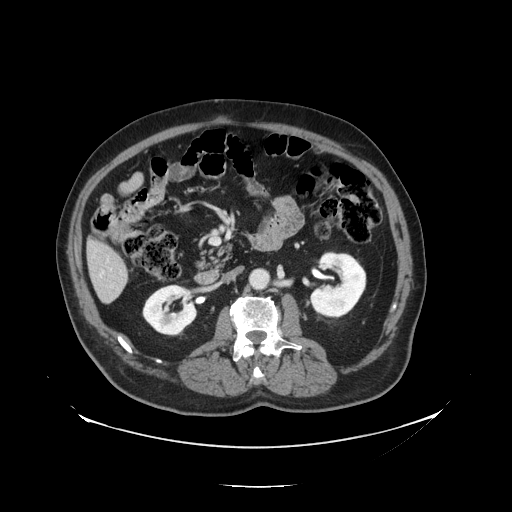
Contrast-enhanced abdominal CT, one axial slice; position 45 of 138 along the scan axis; reconstruction kernel STANDARD; intravenous contrast given; soft-tissue window (W 400 / L 40 HU); 512 × 512 image matrix. Male patient, age 77 years. From the clinical record (not read from this slice): diagnosis: colorectal cancer liver metastases, imaged before liver resection; multiple liver metastases: no; largest metastasis: 1.5 cm; disease in both lobes: no.
Annotated regions visible in this slice (expert manual segmentation):
- liver: bounding box (x1, y1, x2, y2) in pixels: (89, 242, 129, 303)
- planned liver remnant (the part of the liver to remain after resection): (88, 241, 126, 277)